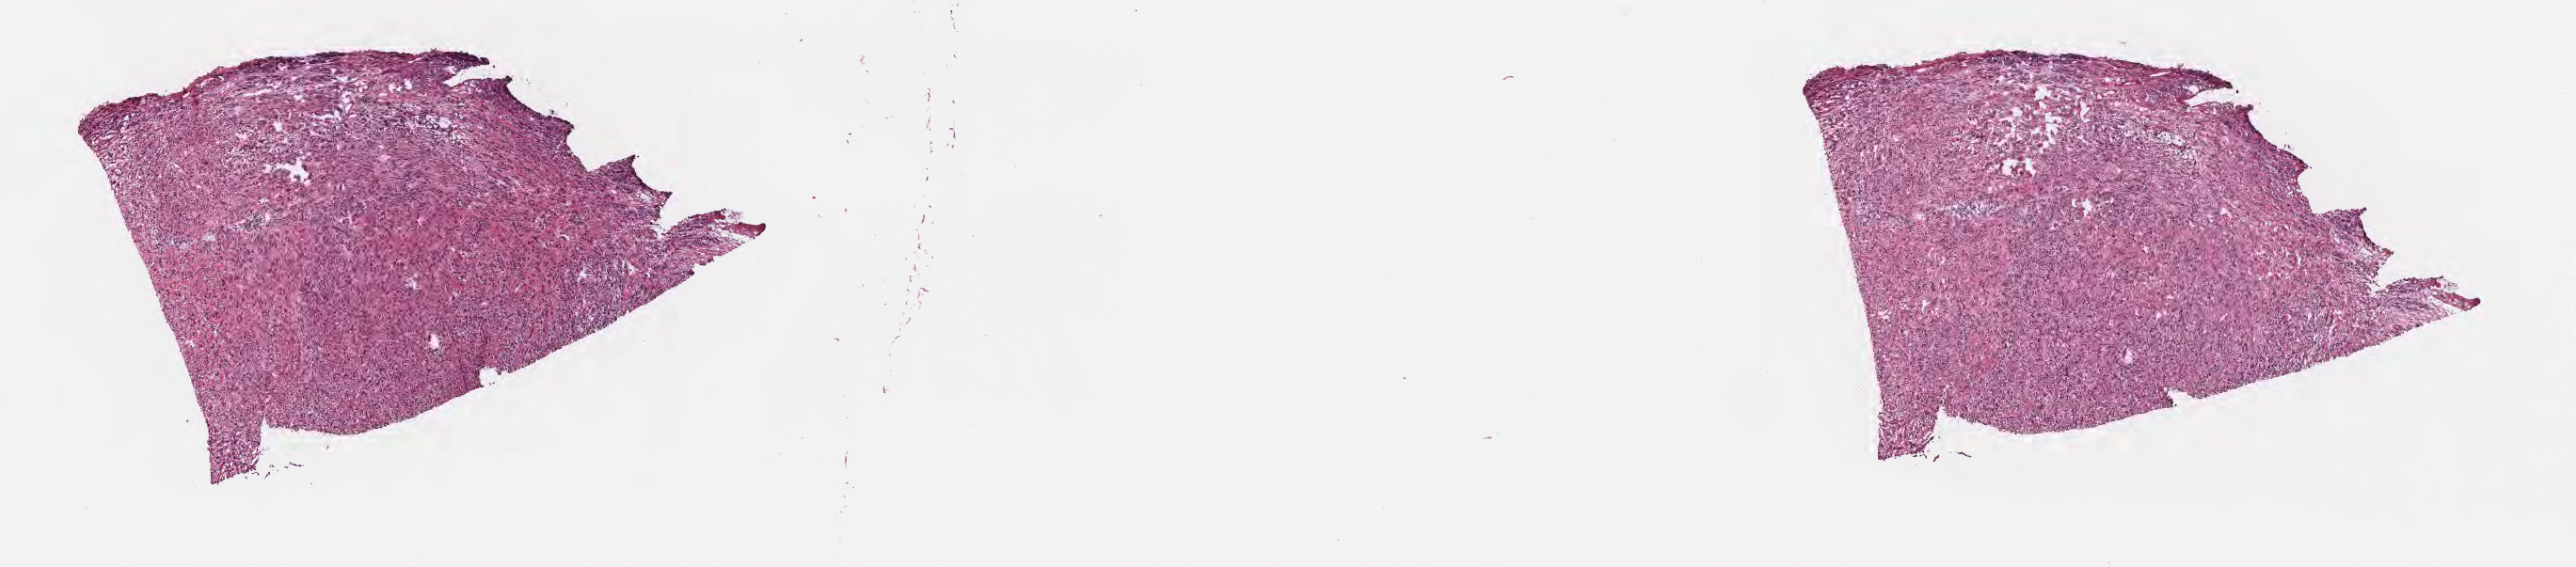
Whole-slide image, hematoxylin and eosin (H&E) stain, low-resolution overview of the scanned area, about 22.1 x 4.9 mm; cryosection; metastatic tumor tissue, resected from lymph node. Patient: female, age at initial diagnosis 39 years. Slide review estimates, as recorded: tumor cells 53%, tumor nuclei 92%, stromal cells 47%, necrosis 0%, normal cells 0%. Infiltration values recorded for this section: lymphocyte infiltration 5%, monocyte infiltration 0%, neutrophil infiltration 0%.
- patient diagnosis (primary): Atypical carcinoid tumor
- section: bottom of the tissue portion